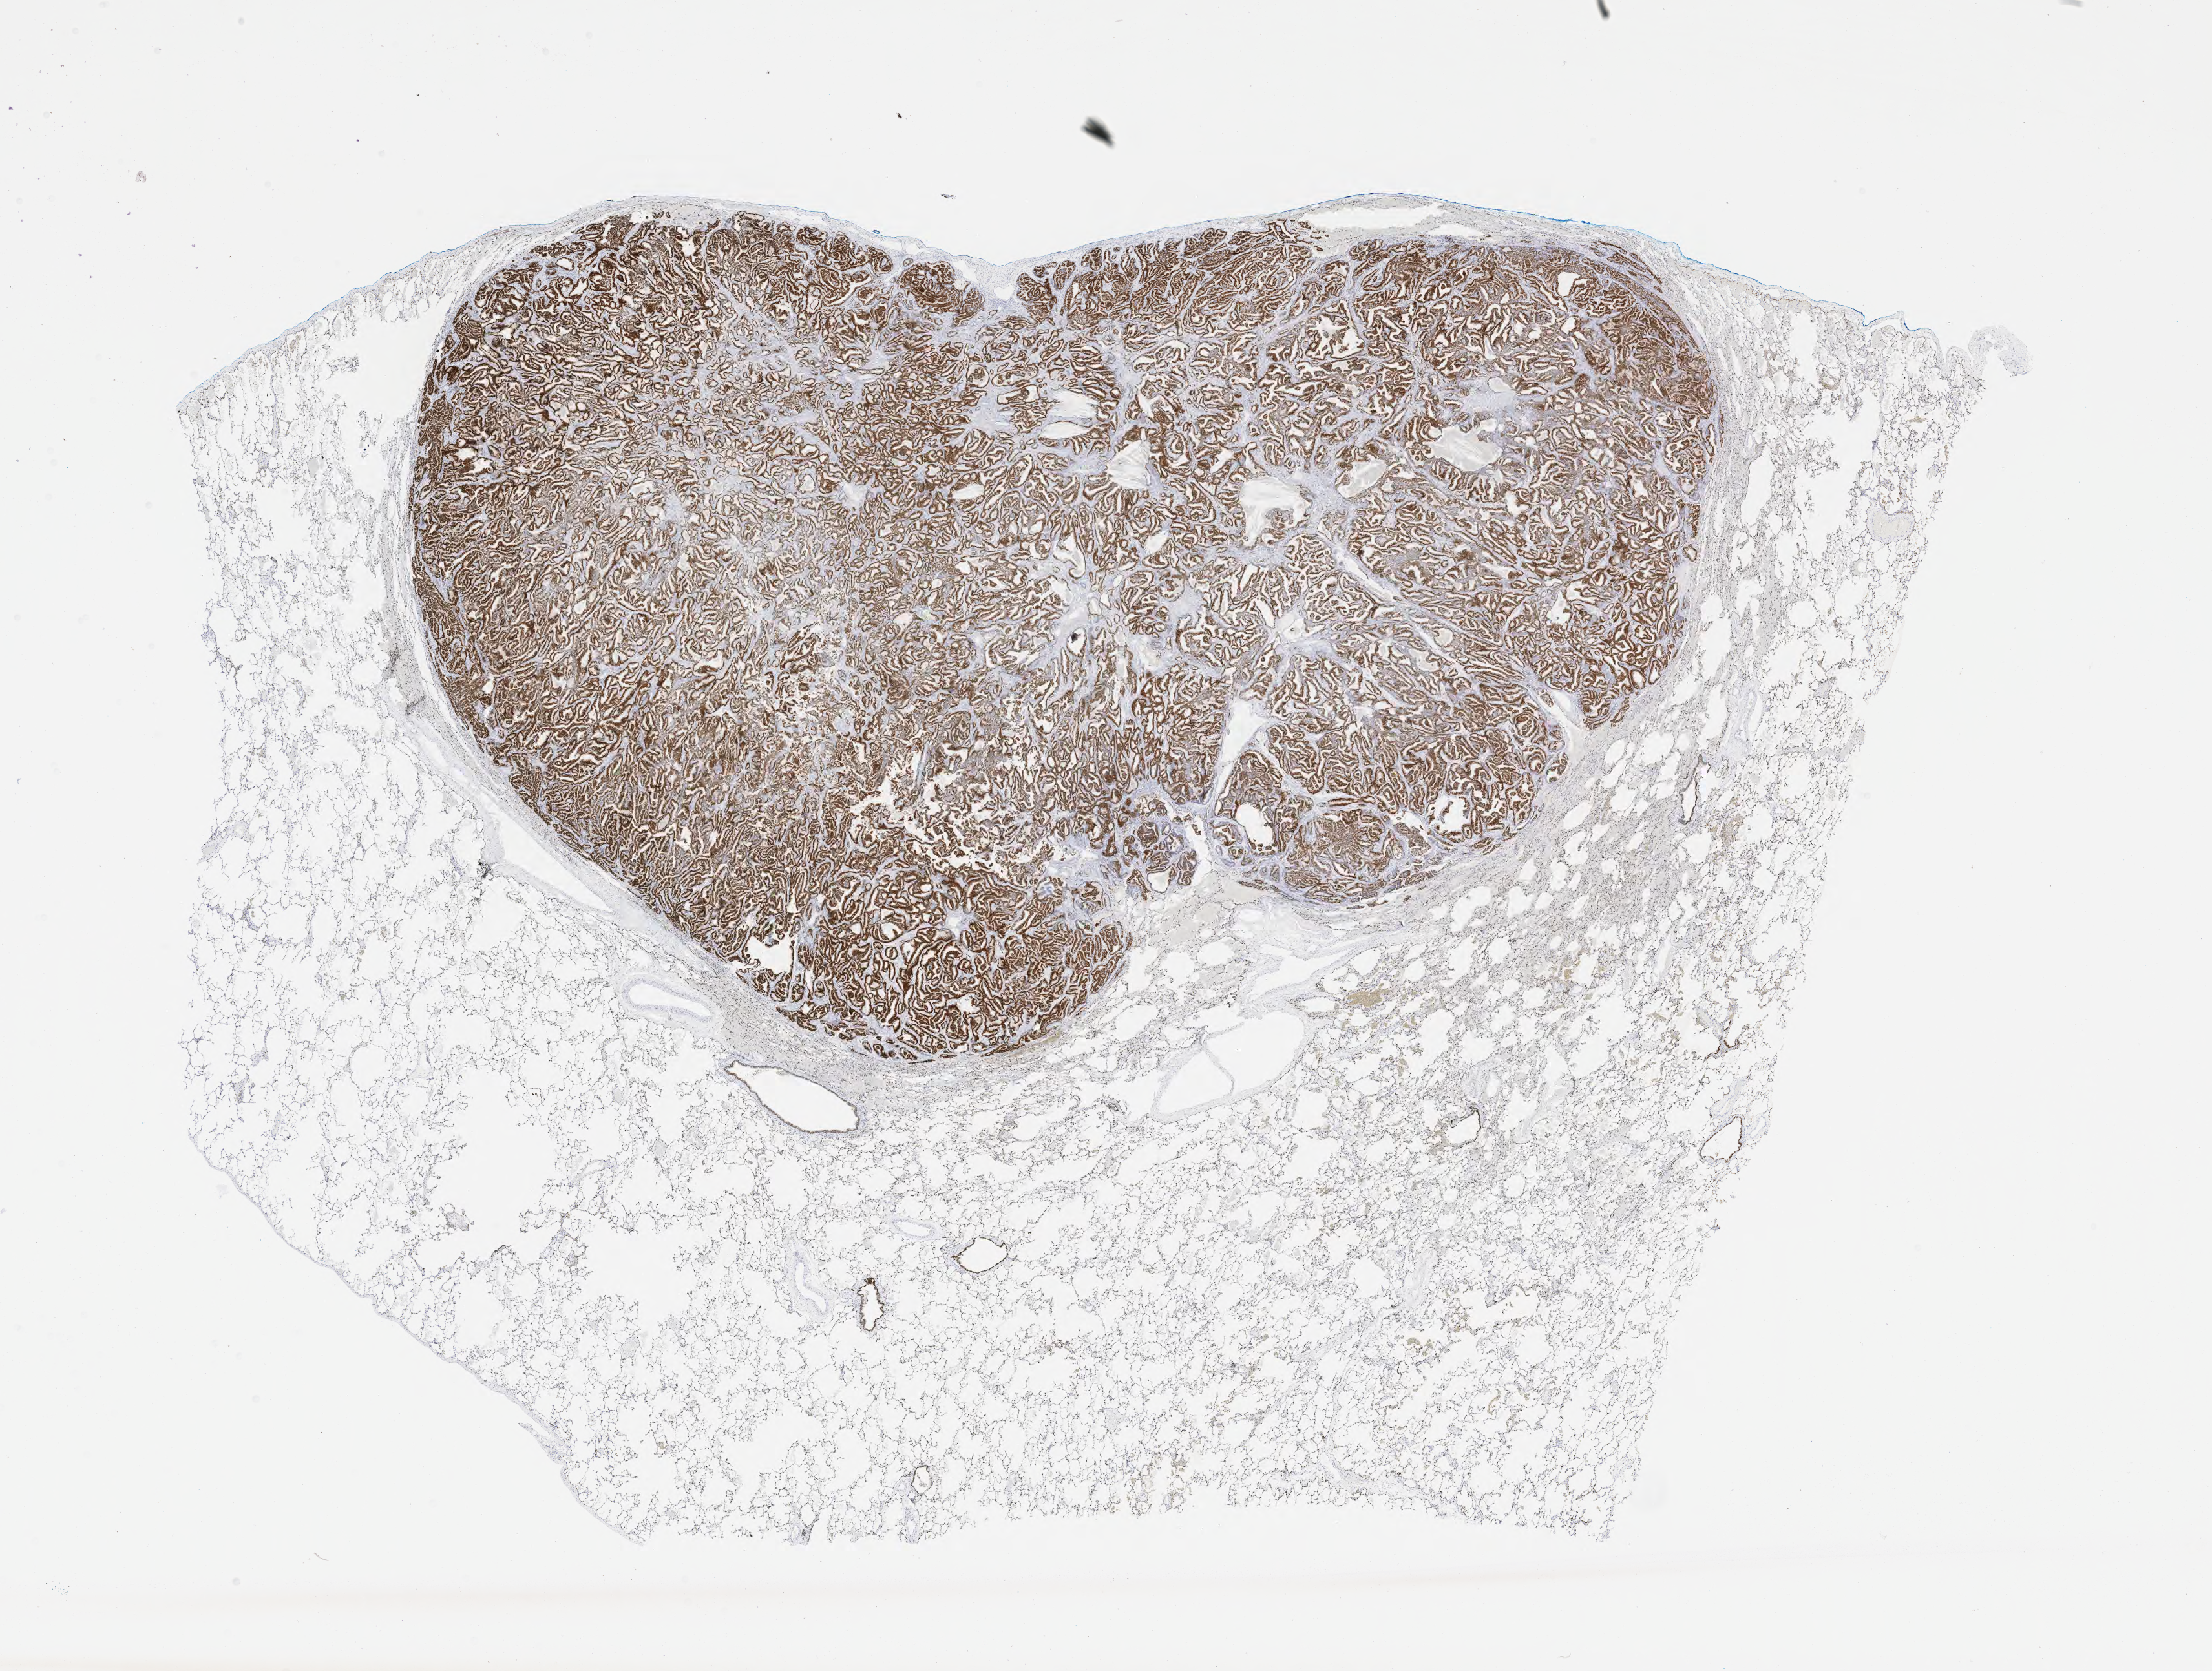
Whole-slide image, immunohistochemical stain for TTF-1 (thyroid transcription factor 1) — whole scanned area (about 27.7 x 20.9 mm) shown as a low-resolution overview, specimen: tumor tissue, site: lung. Patient sex: female.
• histologic diagnosis: Adenocarcinoma, NOS